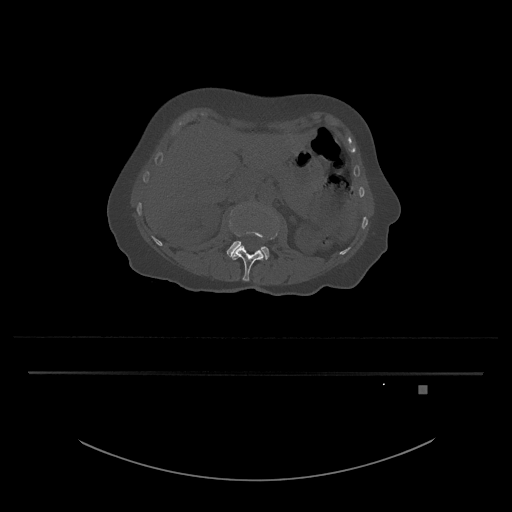
CT including the spine, one axial slice; slice 469 of 797 in the series (ordered by position); 120 kVp; bone window (W 1800 / L 400 HU); 0.5 mm slice thickness; 512 × 512 image matrix. Patient: female, 57 years. Case-level facts recorded for this patient, not image findings: primary cancer: cervical.
Annotated regions visible in this slice (semi-automatically segmented with operator editing):
- L3 vertebra: box from (x=226, y=205) to (x=279, y=260) px